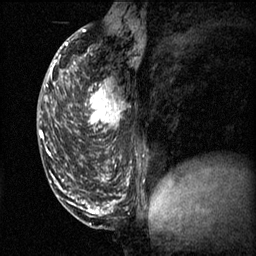
Breast MRI (dynamic contrast-enhanced), one sagittal slice; position 28 of 60 along the scan axis; 3 images stored at this slice position (order not interpretable as contrast timing); 1.5 T; TE 4.2 ms, TR 11.1 ms; 2 mm slice thickness; 256 × 256 image matrix. Female patient, age 50 years.
Structures marked on this image (semi-automatically segmented with operator editing):
- analysis volume of interest (the breast-tissue region the enhancement analysis was run in; not a lesion): bounding box [x1, y1, x2, y2] px = [68, 68, 135, 141]
- tumour enhancement mask (voxels above the 70 % enhancement threshold inside the analysis volume of interest): [74, 68, 126, 141]